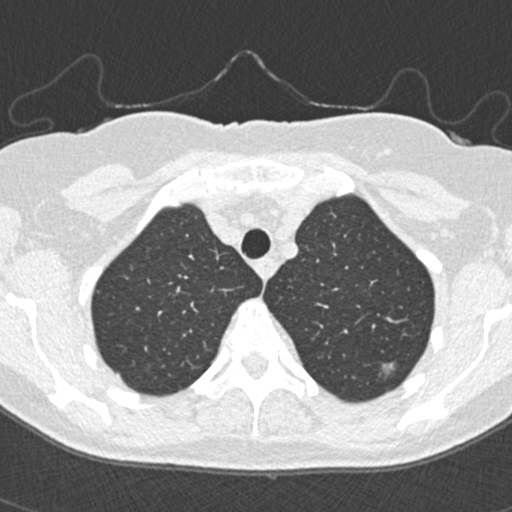
Low-dose screening chest CT, one axial slice; lung window (W 1500 / L -600 HU); 1 mm slice thickness; 512 × 512 image matrix, field of view 298 × 298 mm.
Outlined on this slice (expert manual segmentation):
- lesion 2 (tumor, upper lobe of left lung): bounding box <383,362,395,376> (left, top, right, bottom; pixels)